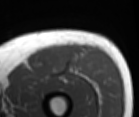
MRI of an extremity soft-tissue mass, one axial slice. Slice 38 of 86 in the series (ordered by position). MR volume resampled by the dataset authors to the PET/CT grid (not the native acquisition matrix). 139 × 117 image matrix, field of view 136 × 114 mm. Male patient. Case-level facts recorded for this patient, not image findings: histological type: extraskeletal osteosarcoma; grade: high; site of the primary tumour: thigh.
Annotated regions visible in this slice (expert contour drawn on MRI and transferred to this co-registered scan by the dataset authors):
- gross tumour volume (mass): bounding box <63,48,84,74> (left, top, right, bottom; pixels)